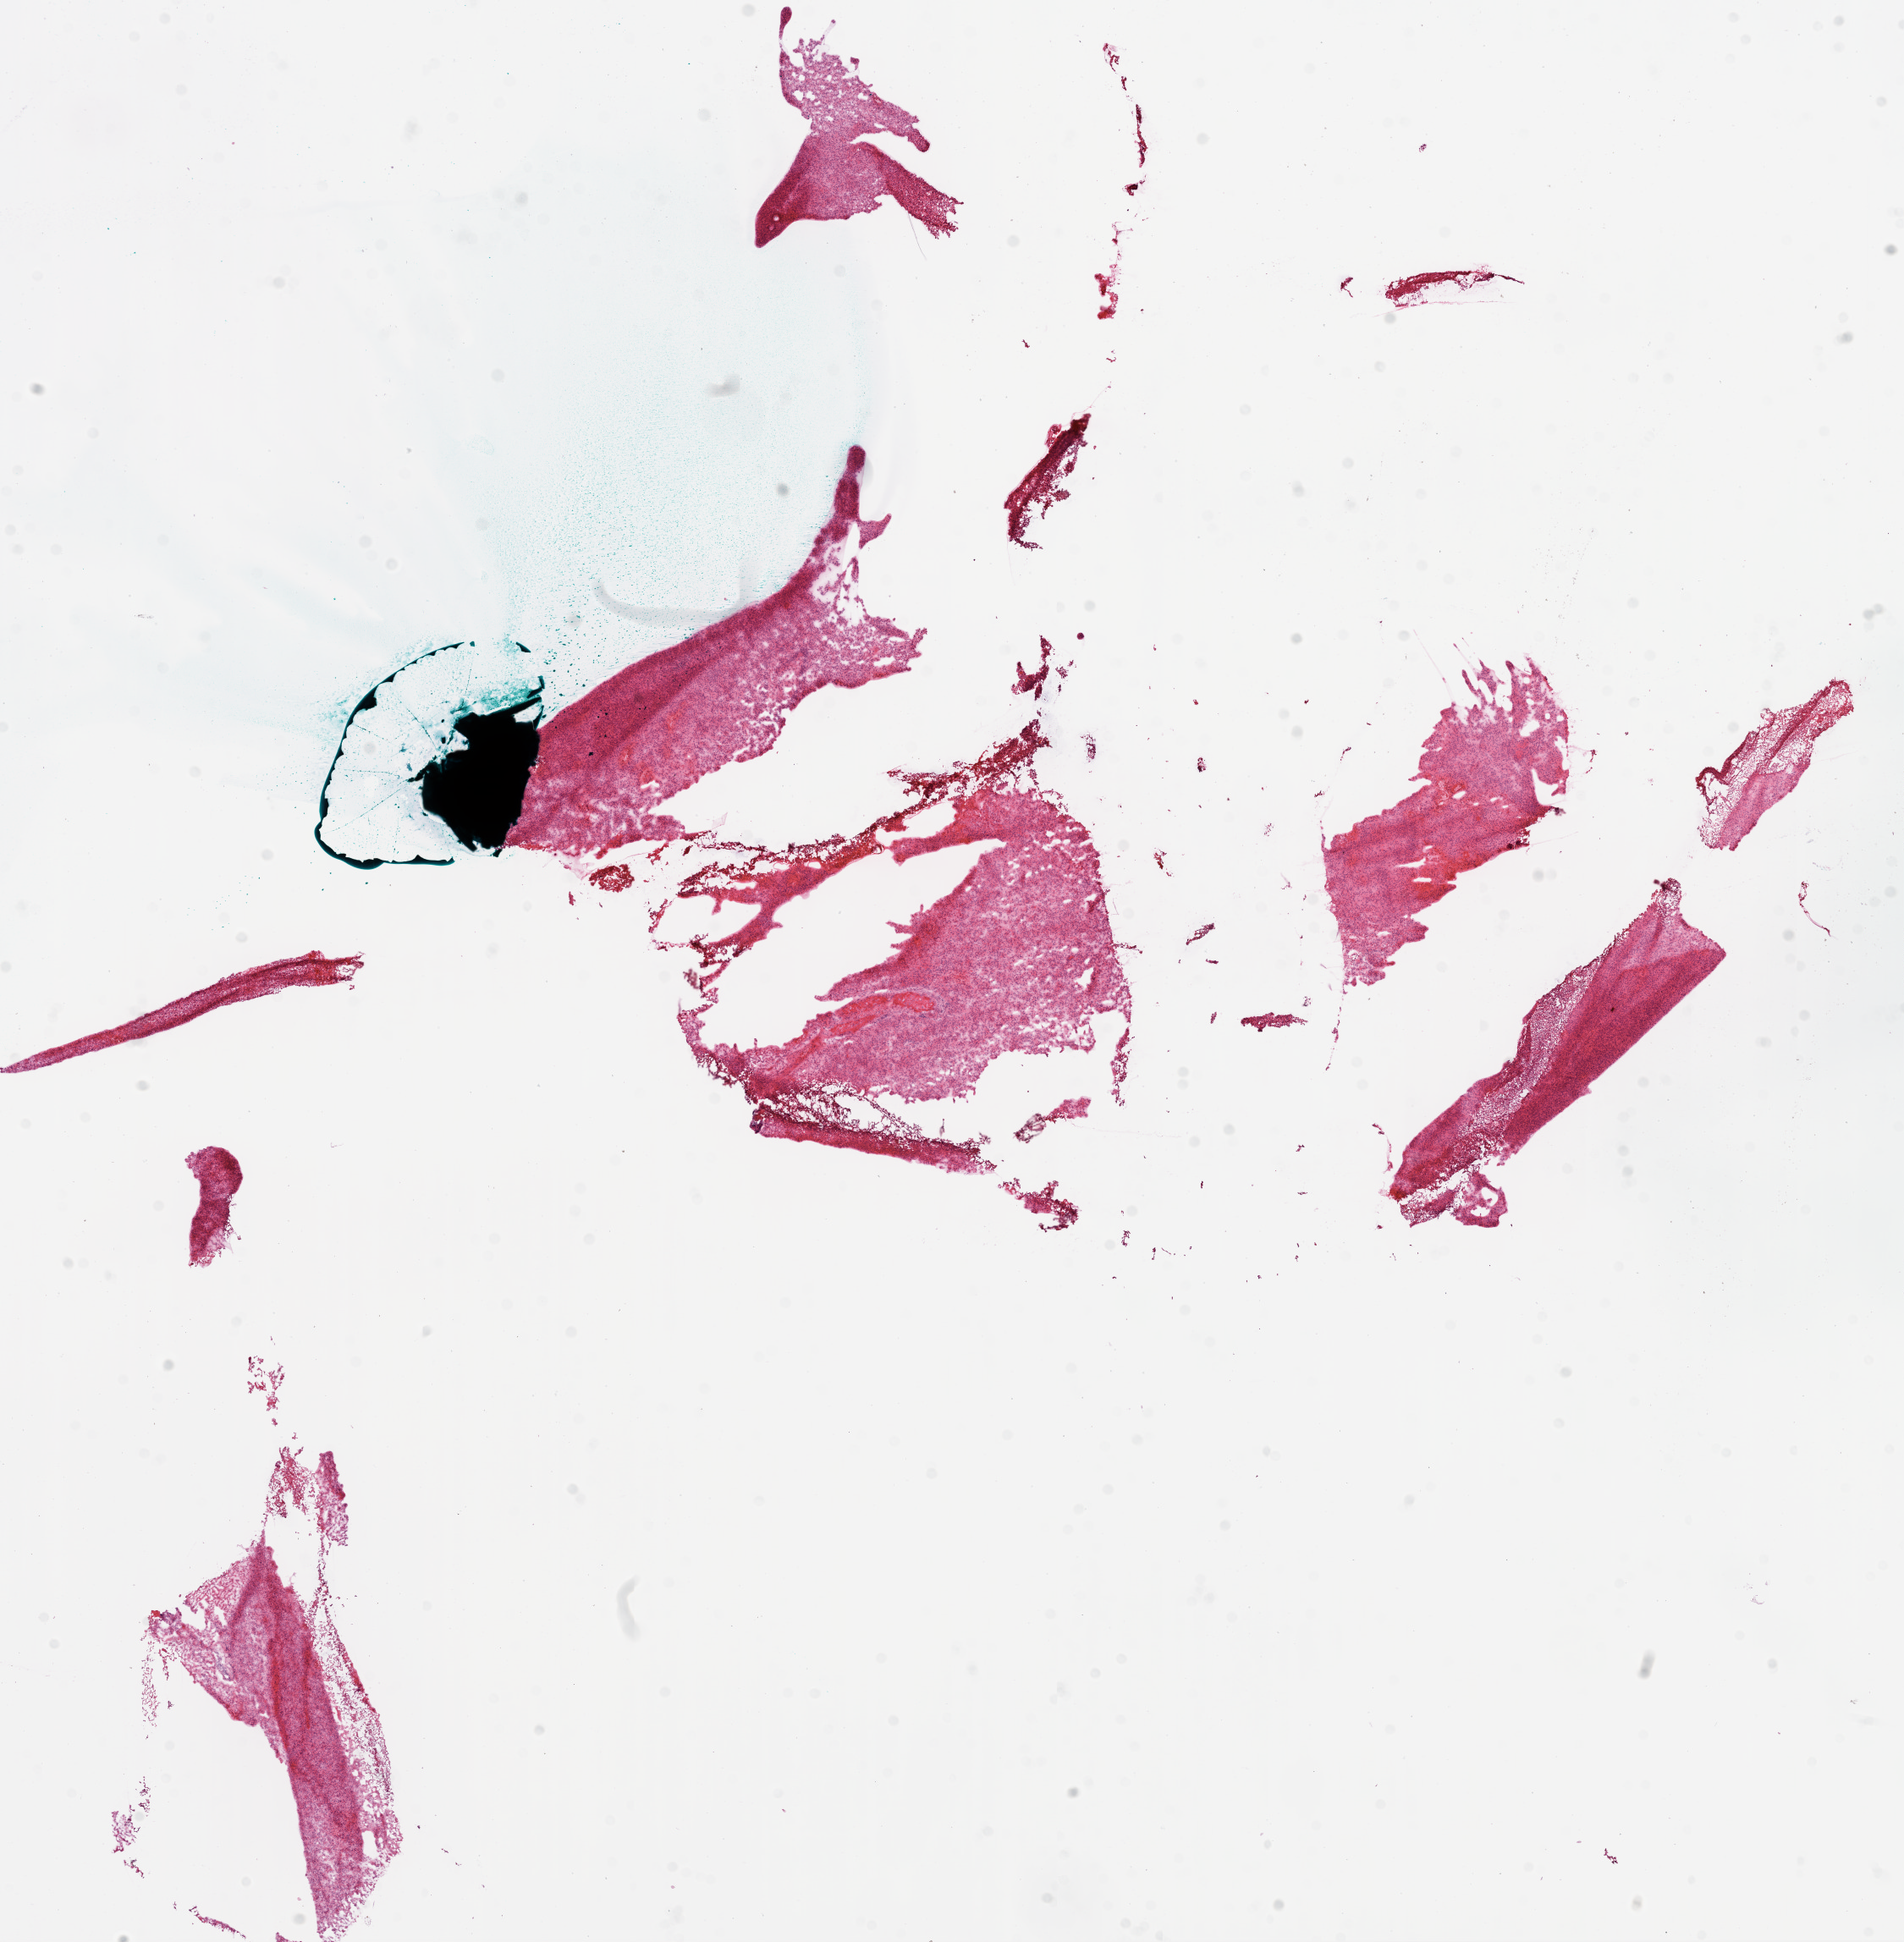
Hematoxylin and eosin (H&E) stained whole-slide image — a low-resolution overview of the entire scanned area, about 18.1 x 18.4 mm (from a 20x scan); frozen section; sample: primary tumour, brain. Patient: male, age at initial diagnosis 60 years. Pathologist review of this section (percent, as recorded): tumour cells 95%, tumour nuclei 100%, normal cells 0%, stromal cells 0%, necrosis 5%.
Pathologic diagnosis: Glioblastoma.